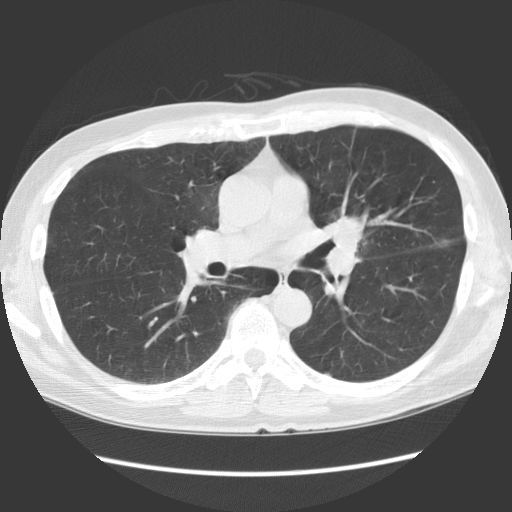
Low-dose screening chest CT, one axial slice. 140 kVp. Lung window (W 1500 / L -600 HU). 2.5 mm slice thickness. 512 × 512 image matrix, field of view 360 × 360 mm.
Outlined on this slice (outlined manually by an expert reader):
- lesion 1 (tumor, hilum of left lung): box from (x=326, y=212) to (x=366, y=256) px